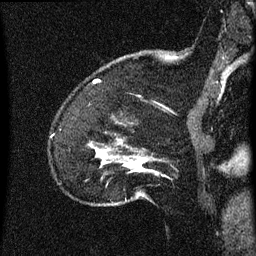
Breast MRI (dynamic contrast-enhanced), one sagittal slice. Position 11 of 60 along the scan axis. Dynamic contrast-enhanced series, image 2 of 3 at this slice position (ordered by acquisition). 1.5 T. TE 4.2 ms, TR 8 ms. 2 mm slice thickness. 256 × 256 image matrix, field of view 180 × 180 mm. Female patient, age 52 years.
Annotated regions visible in this slice (semi-automatic segmentation, software-assisted and operator-edited):
- analysis volume of interest (the breast-tissue region the enhancement analysis was run in; not a lesion): bounding box (x1, y1, x2, y2) in pixels: (89, 118, 152, 207)
- tumour enhancement mask (voxels above the 70 % enhancement threshold inside the analysis volume of interest): (96, 150, 146, 173)